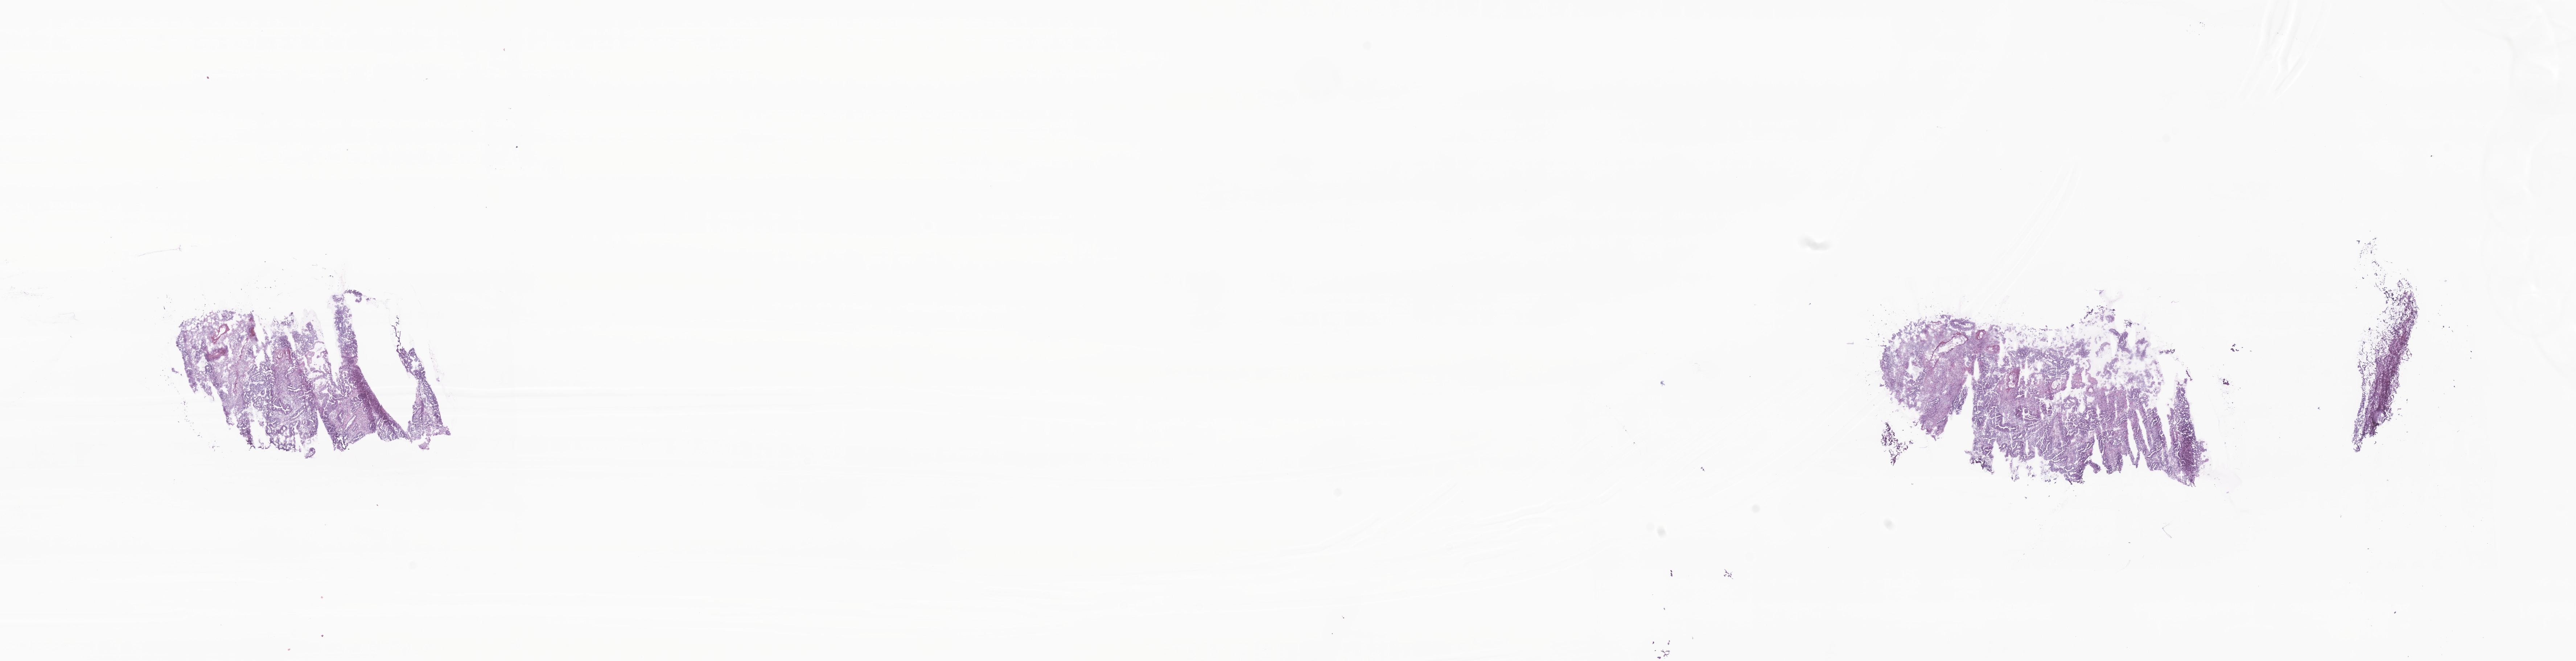
Whole-slide image, hematoxylin and eosin (H&E) stain — low-resolution overview of the scanned area, about 29.9 x 7.7 mm; frozen section; primary tumor; site: ascending colon. Female, age 73 years at initial diagnosis. Pathologist review of this section (percent, as recorded): tumor cells 100%, tumor nuclei 75%, stromal cells 0%, necrosis 0%, normal cells 0%. Inflammatory infiltration, as recorded: lymphocyte infiltration 0%, monocyte infiltration 0%, neutrophil infiltration 0%.
• diagnosis: Mucinous adenocarcinoma